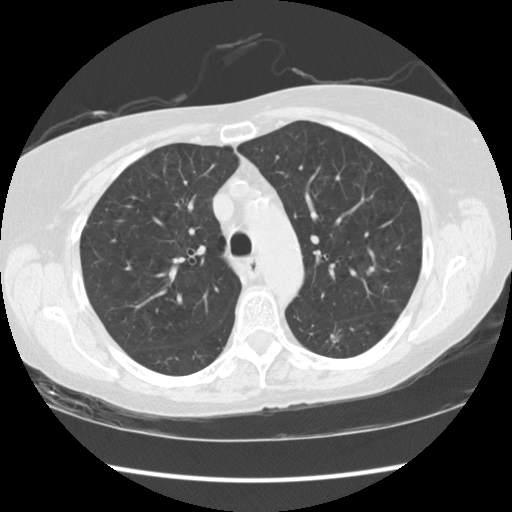
Chest CT (low-dose screening protocol), one axial image; third annual screen; lung window (W 1500 / L -600 HU); 2.5 mm slice thickness; standard (soft-tissue) reconstruction kernel (STANDARD). Female, age 63 years at enrolment. Current smoker at enrolment.
Lesion marked by an expert reader, box from (x=312, y=316) to (x=355, y=358) px. The screening reader recorded 4 non-calcified nodules or masses ≥4 mm on this exam (left lower lobe, right upper lobe, left upper lobe, left lower lobe); which of them this box marks is not recorded. Official screen result: positive, other. Lung cancer was diagnosed 60 days after this screen: squamous cell carcinoma, NOS, left lower lobe, moderately differentiated (G2), stage IB (AJCC 6th edition), 15 mm at pathology.